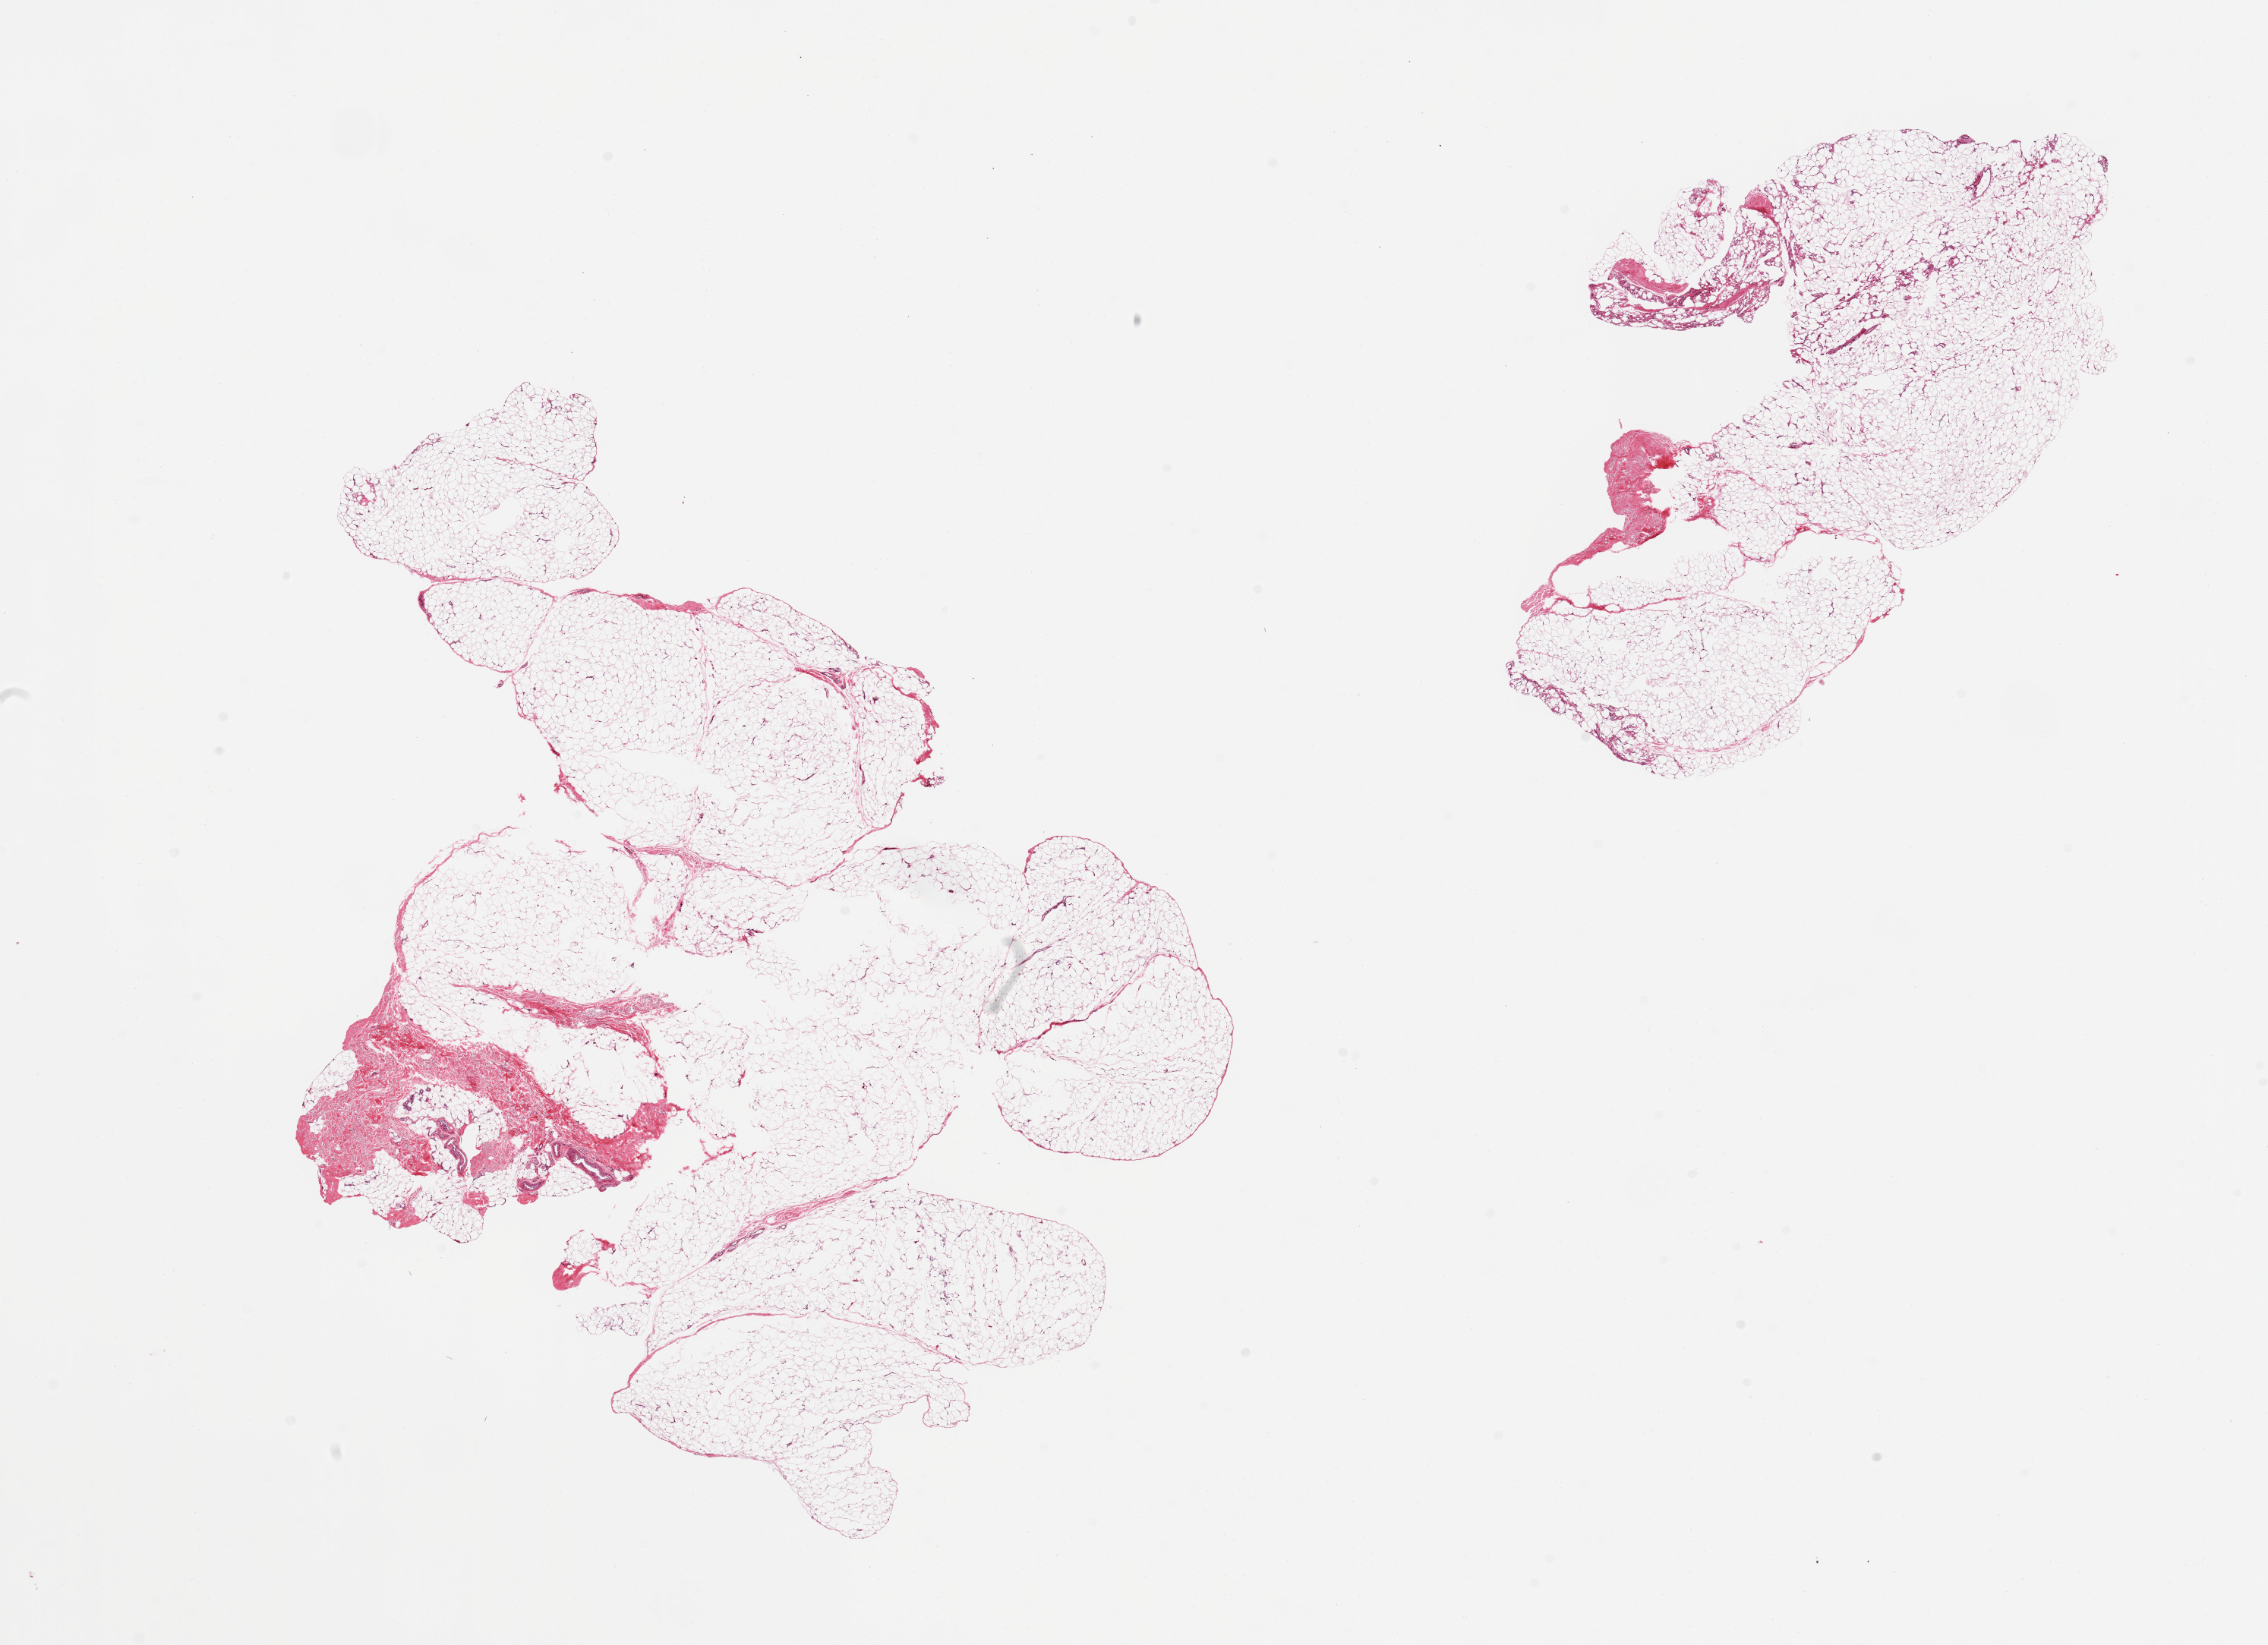
Whole-slide image, H&E stain, low-resolution overview of the scanned area, about 23.6 x 17.1 mm (acquisition: 20x scan). PAXgene-fixed, paraffin-embedded tissue. Target tissue: adipose tissue. Donor tissue sample. Female donor.
* review note (as recorded): 2 pieces ~10% fibrofascial tissue